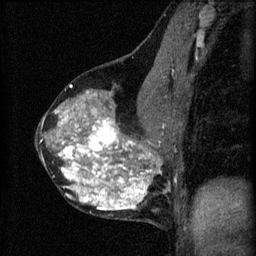
Breast MRI (dynamic contrast-enhanced), one sagittal slice; slice 34 of 60 in the series (ordered by position); 3 images stored at this slice position (order not interpretable as contrast timing); 1.5 T; TE 4.2 ms, TR 8.2 ms; 2 mm slice thickness; 256 × 256 image matrix. Female patient, age 40 years.
Outlined on this slice (semi-automatic segmentation, software-assisted and operator-edited):
- analysis volume of interest (the breast-tissue region the enhancement analysis was run in; not a lesion): box from (x=36, y=76) to (x=179, y=219) px
- tumour enhancement mask (voxels above the 70 % enhancement threshold inside the analysis volume of interest): (x=58, y=92)–(x=165, y=211)